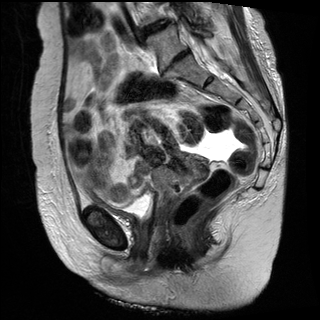
Pelvic MRI for cervical cancer, one sagittal slice; slice 15 of 30 in the series (ordered by position); T2-weighted; 1.5 T; TE 89 ms, TR 2930 ms; 320 × 320 image matrix. Female patient, age 61 years.
Annotated regions visible in this slice (expert manual segmentation):
- uterus and cervix: box from (x=131, y=117) to (x=211, y=208) px